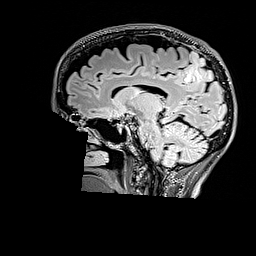
Brain MRI from a brain-tumour surgery series, one sagittal slice; slice 100 of 176 in the series (ordered by position); T2 FLAIR; 256 × 256 image matrix, field of view 256 × 256 mm. From the clinical record (not read from this slice): histopathology: Astrocytoma; WHO grade: 3; IDH mutation: yes; tumour location: Right Parietal.
Annotated regions visible in this slice (expert manual segmentation):
- tumour: bounding box <184,57,214,83> (left, top, right, bottom; pixels)
- tumour: <185,51,214,82>